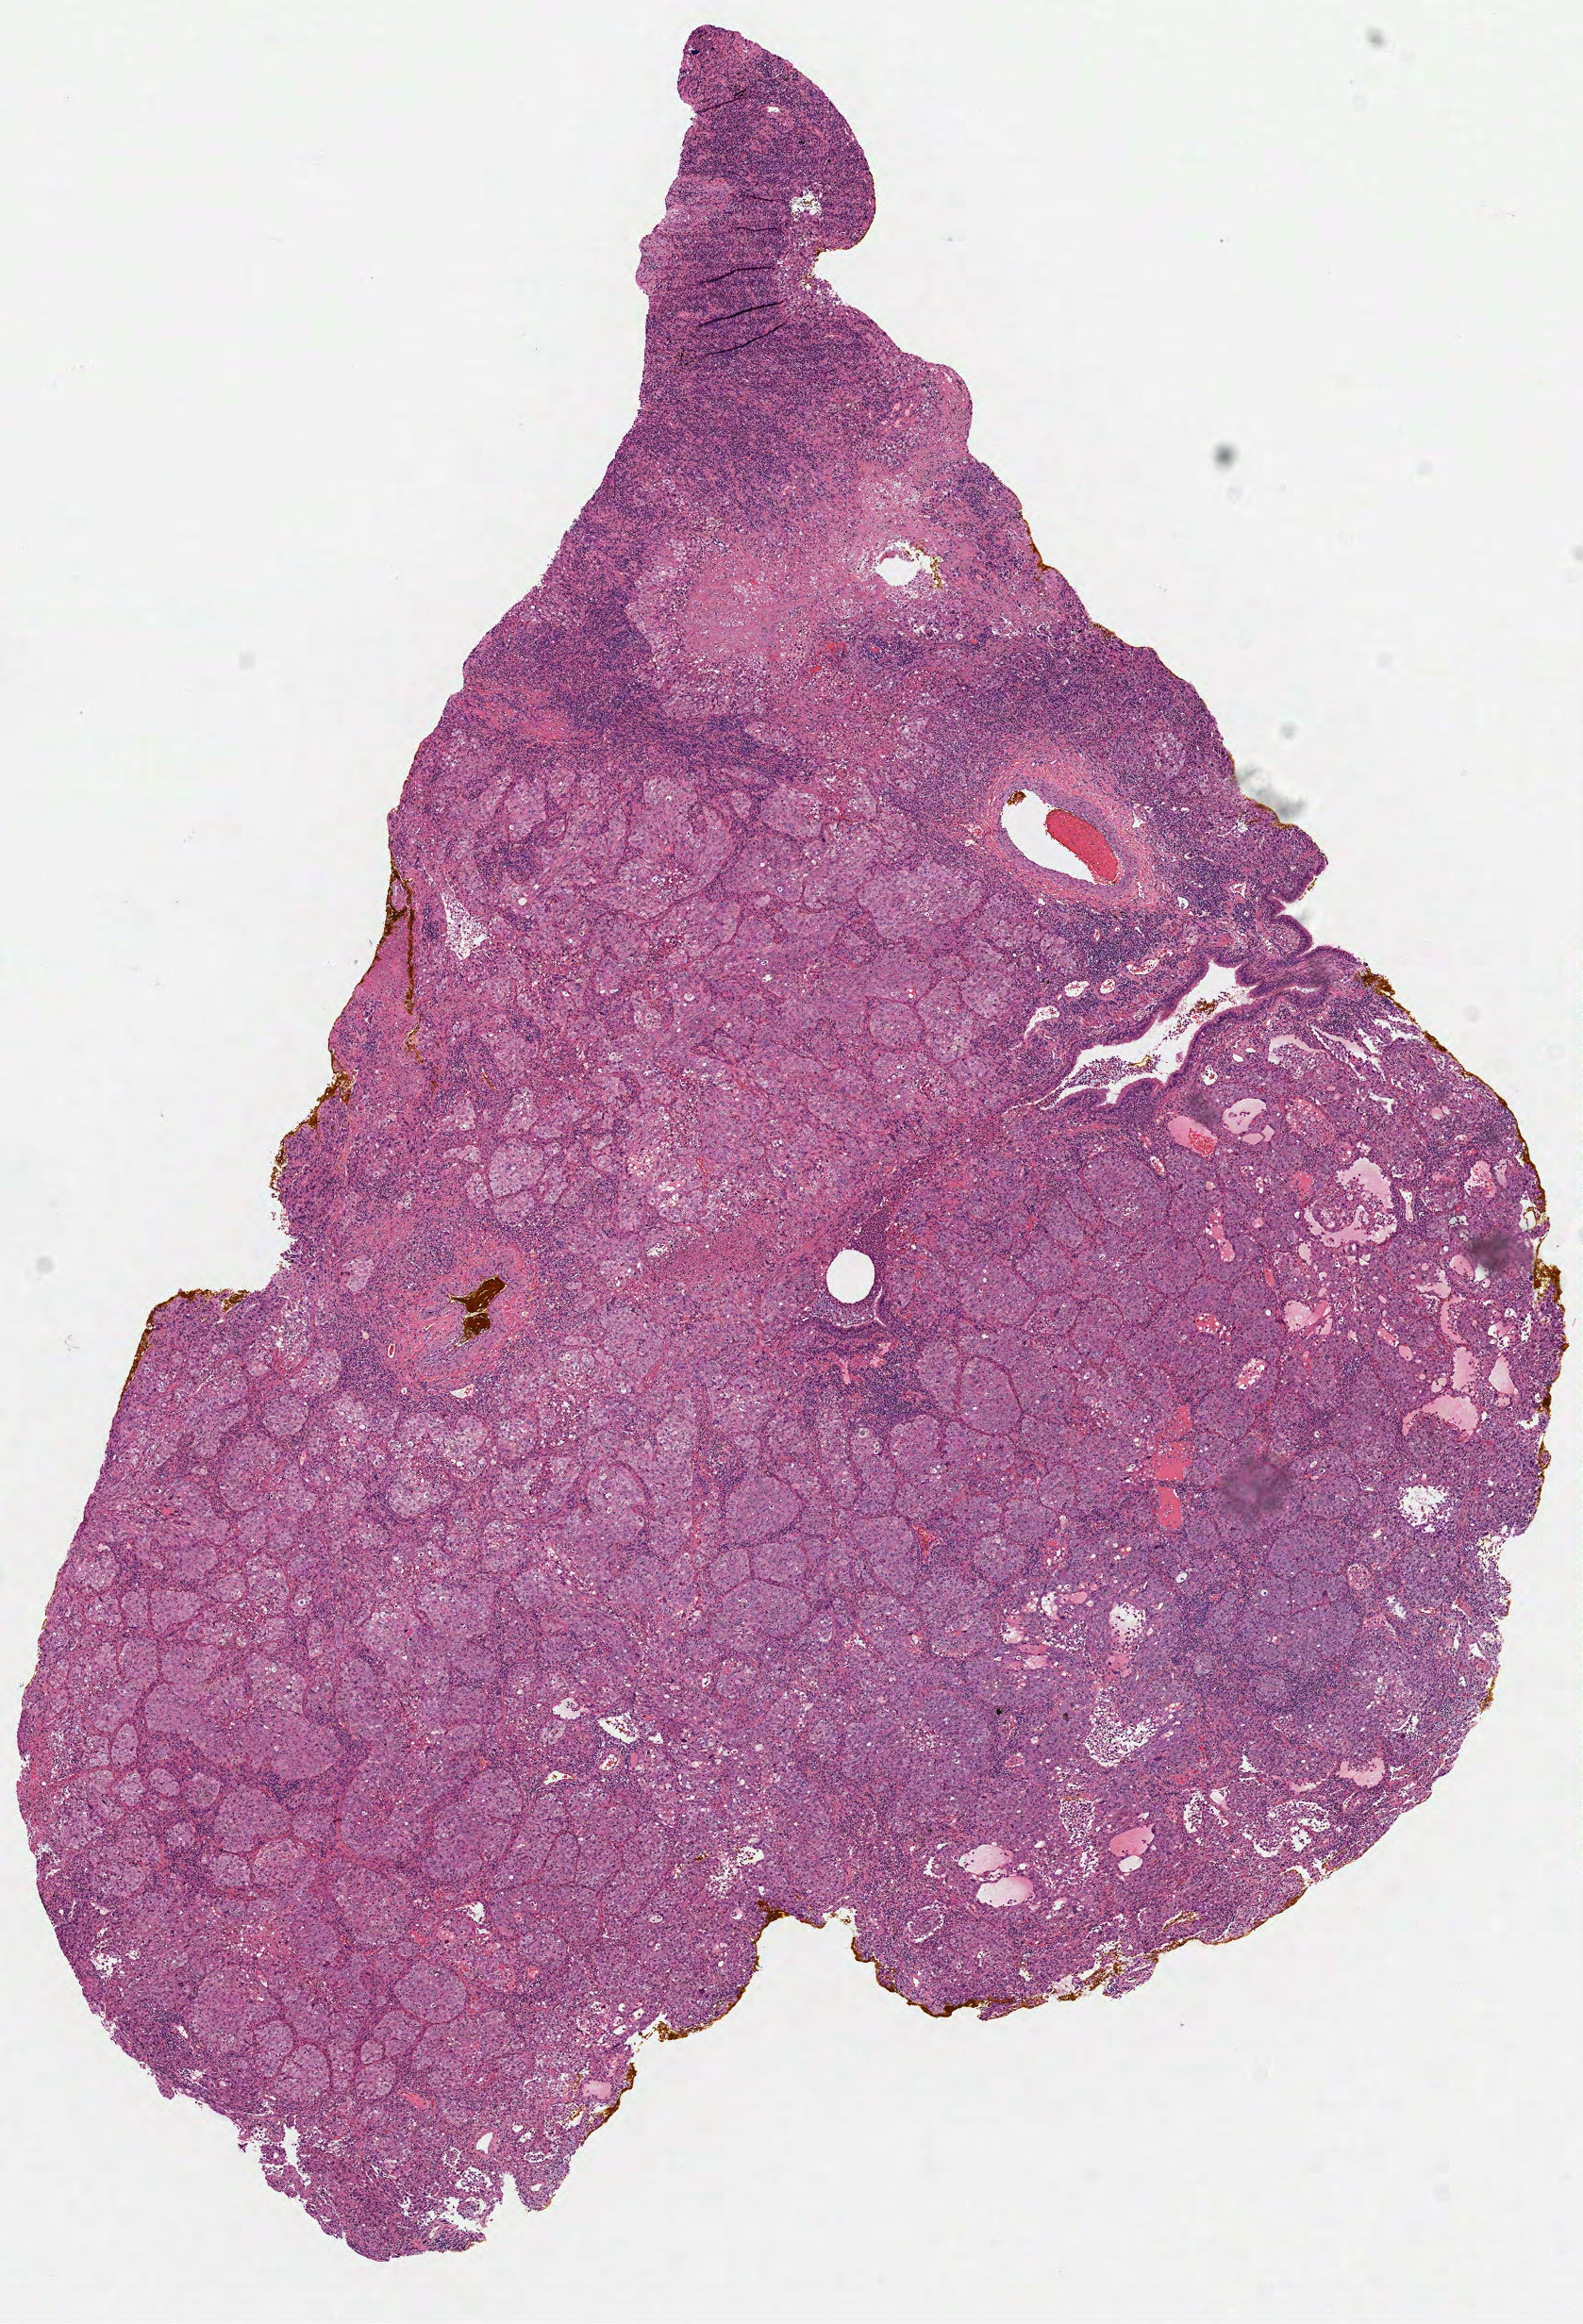
Whole-slide histology image, H&E-stained, low-resolution overview of the scanned area, about 6.8 x 9.9 mm; FFPE section; lung, primary tumour sample. Patient: female, age at initial diagnosis 54 years.
Diagnosis: Adenocarcinoma, NOS (upper lobe, lung). AJCC pathologic stage: IB (7th edition). Laterality: right.